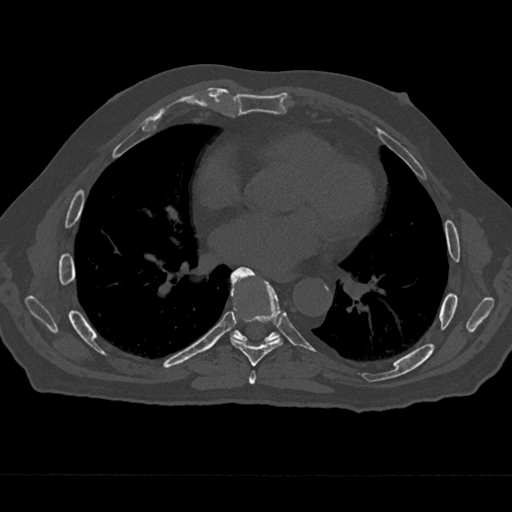
CT including the spine, one axial slice; slice 353 of 797 in the series (ordered by position); 120 kVp; bone window (W 1800 / L 400 HU); 0.5 mm slice thickness; 512 × 512 image matrix, field of view 377 × 377 mm. Patient: male, 75 years. Case-level facts recorded for this patient, not image findings: primary cancer: renal.
Structures marked on this image (semi-automatic segmentation, software-assisted and operator-edited):
- T6 vertebra: bounding box [x1, y1, x2, y2] px = [249, 371, 256, 385]
- T7 vertebra: [230, 267, 283, 366]
- T8 vertebra: [230, 278, 280, 343]